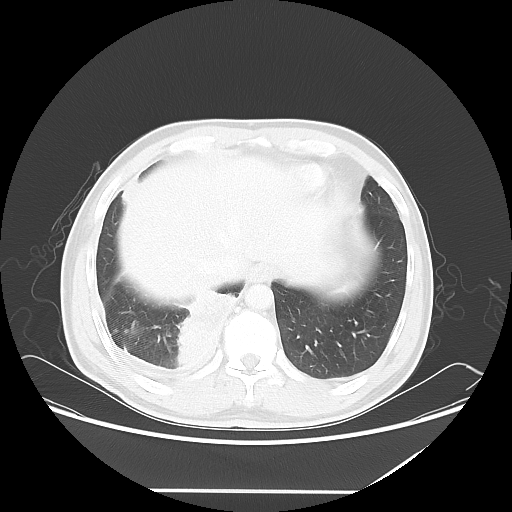
Chest CT, one axial slice. Slice 15 of 60 in the series (ordered by position). Reconstruction kernel LUNG. Lung window (W 1500 / L -600 HU). 5 mm slice thickness. 512 × 512 image matrix, field of view 419 × 419 mm. Male patient, age 48 years. From the clinical record (not read from this slice): clinical TNM (as recorded): T3 N3 M1a.
Structures marked on this image (rectangle marked by the reading radiologist):
- lung tumour (recorded histology: squamous cell carcinoma): bounding box (x1, y1, x2, y2) in pixels: (176, 282, 241, 372)